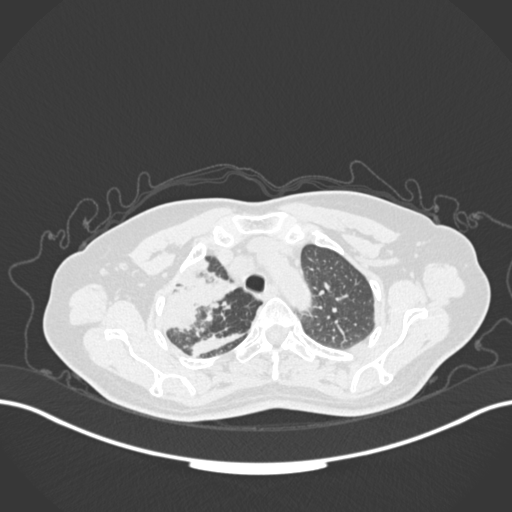
Chest CT, one axial slice. Position 129 of 177 along the scan axis. Lung window (W 1500 / L -600 HU). 1 mm slice thickness. 512 × 512 image matrix, field of view 400 × 400 mm. Patient: female, 60 years. Case-level facts recorded for this patient, not image findings: clinical TNM (as recorded): T3 N1 M1.
Outlined on this slice (bounding box drawn by a radiologist):
- lung tumour (recorded histology: adenocarcinoma): bounding box <153,255,244,337> (left, top, right, bottom; pixels)